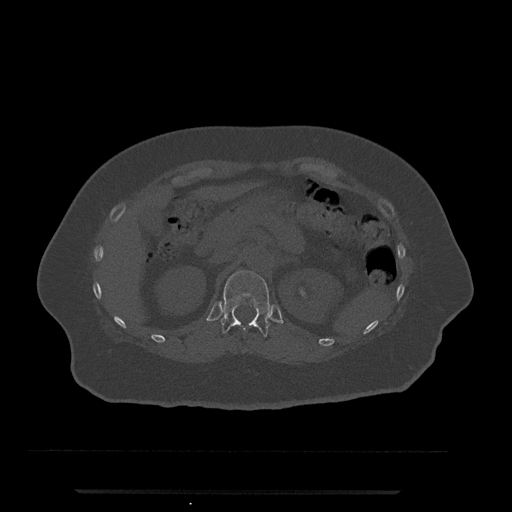
CT including the spine, one axial slice. Position 173 of 797 along the scan axis. Reconstruction kernel Br40s/3. Bone window (W 1800 / L 400 HU). 512 × 512 image matrix. Female patient, age 51 years. Case-level facts recorded for this patient, not image findings: primary cancer: neuro; vertebrae with lytic lesions (as recorded): T8.
Annotated regions visible in this slice (semi-automatic segmentation, software-assisted and operator-edited):
- T12 vertebra: bounding box [x1, y1, x2, y2] px = [221, 270, 270, 338]